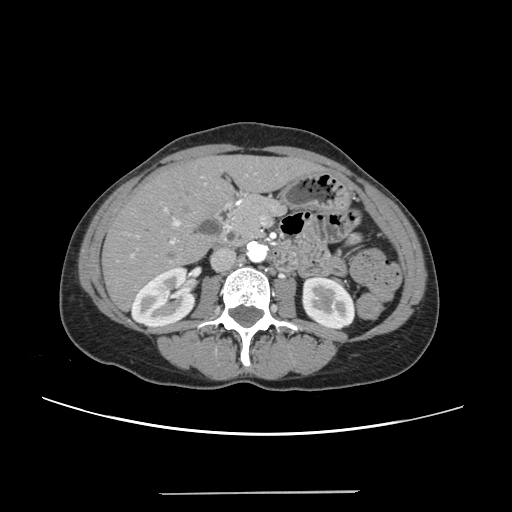
Contrast-enhanced abdominal CT, one axial slice. Position 104 of 240 along the scan axis. 120 kVp. Intravenous contrast given. Soft-tissue window (W 400 / L 40 HU). 512 × 512 image matrix, field of view 371 × 371 mm. Female patient, age 60 years. Case-level facts recorded for this patient, not image findings: diagnosis: colorectal cancer liver metastases, imaged before liver resection; multiple liver metastases: no; largest metastasis: 1.5 cm; chemotherapy before resection: yes.
Structures marked on this image (manually delineated by an expert):
- liver: box from (x=105, y=157) to (x=316, y=308) px
- planned liver remnant (the part of the liver to remain after resection): (x=104, y=158)–(x=317, y=308)
- portal vein (with intrahepatic branches): (x=131, y=174)–(x=248, y=257)